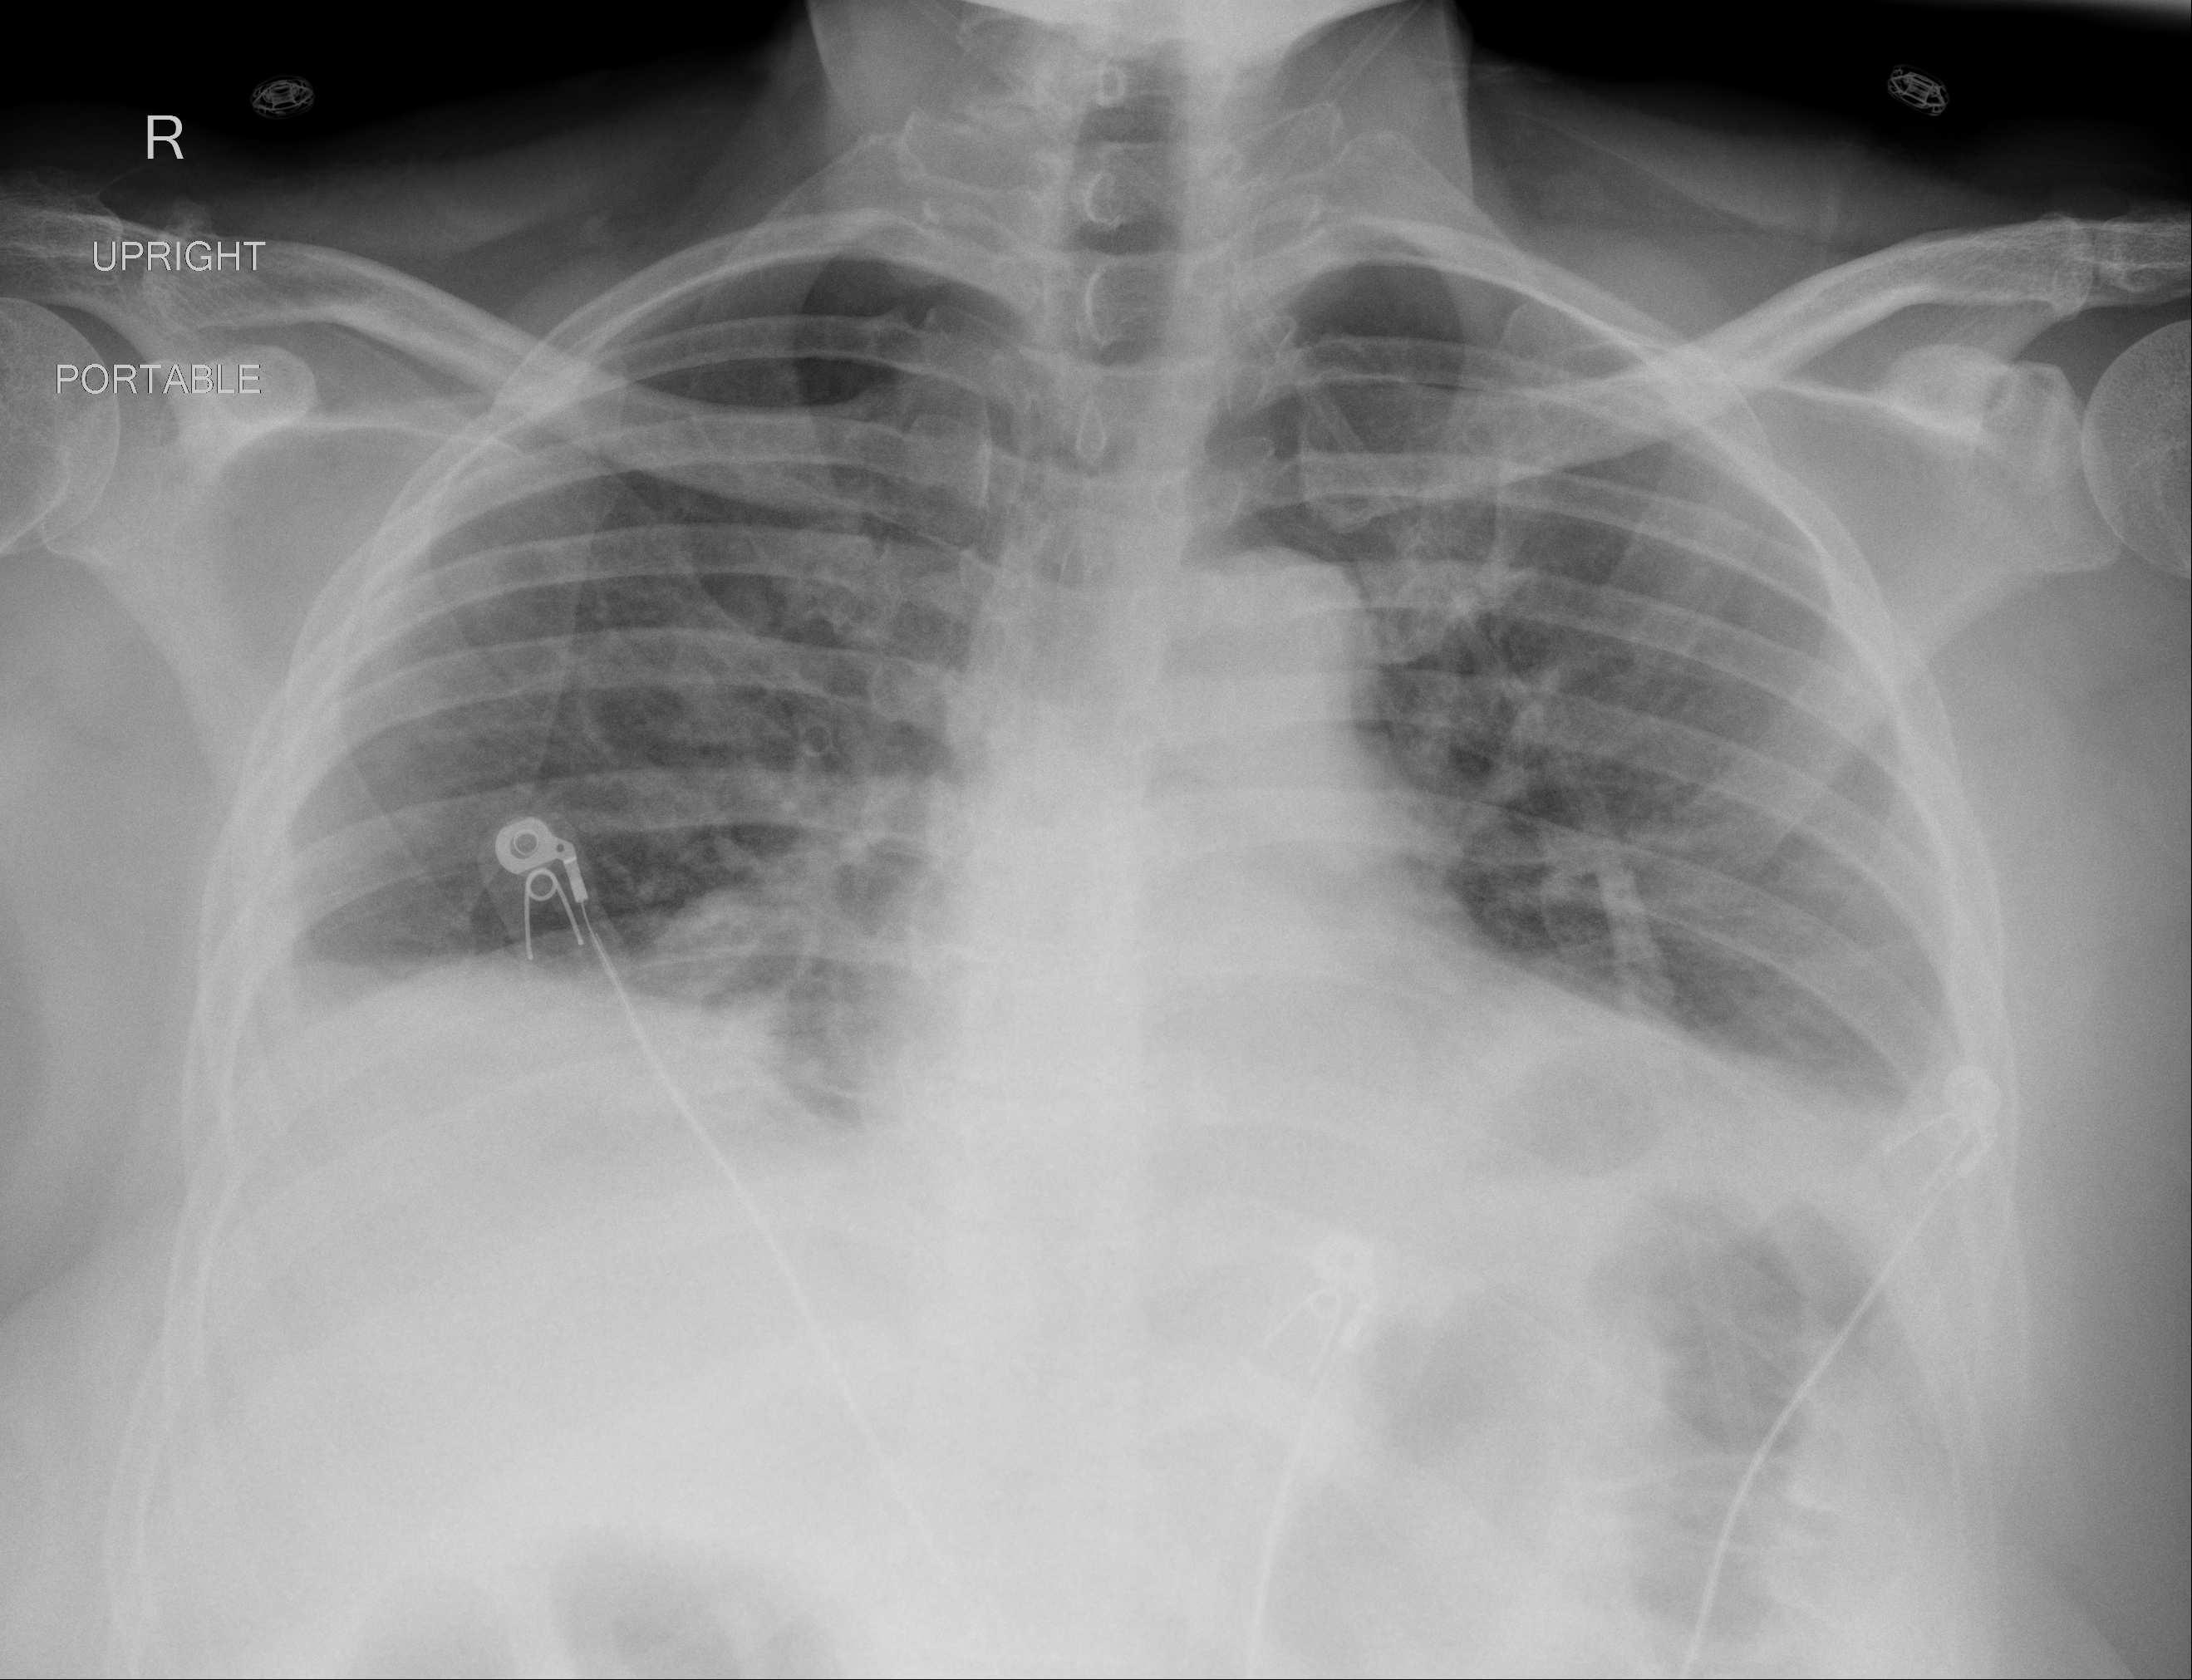
Chest X-ray (portable), AP projection. Female patient, age 57 years; imaged 7 days after the COVID-19 diagnosis.
Radiologist's key findings for this exam: Stable bibasilar streaky opacities are noted with interval blunting of bilateral costophrenic angles.